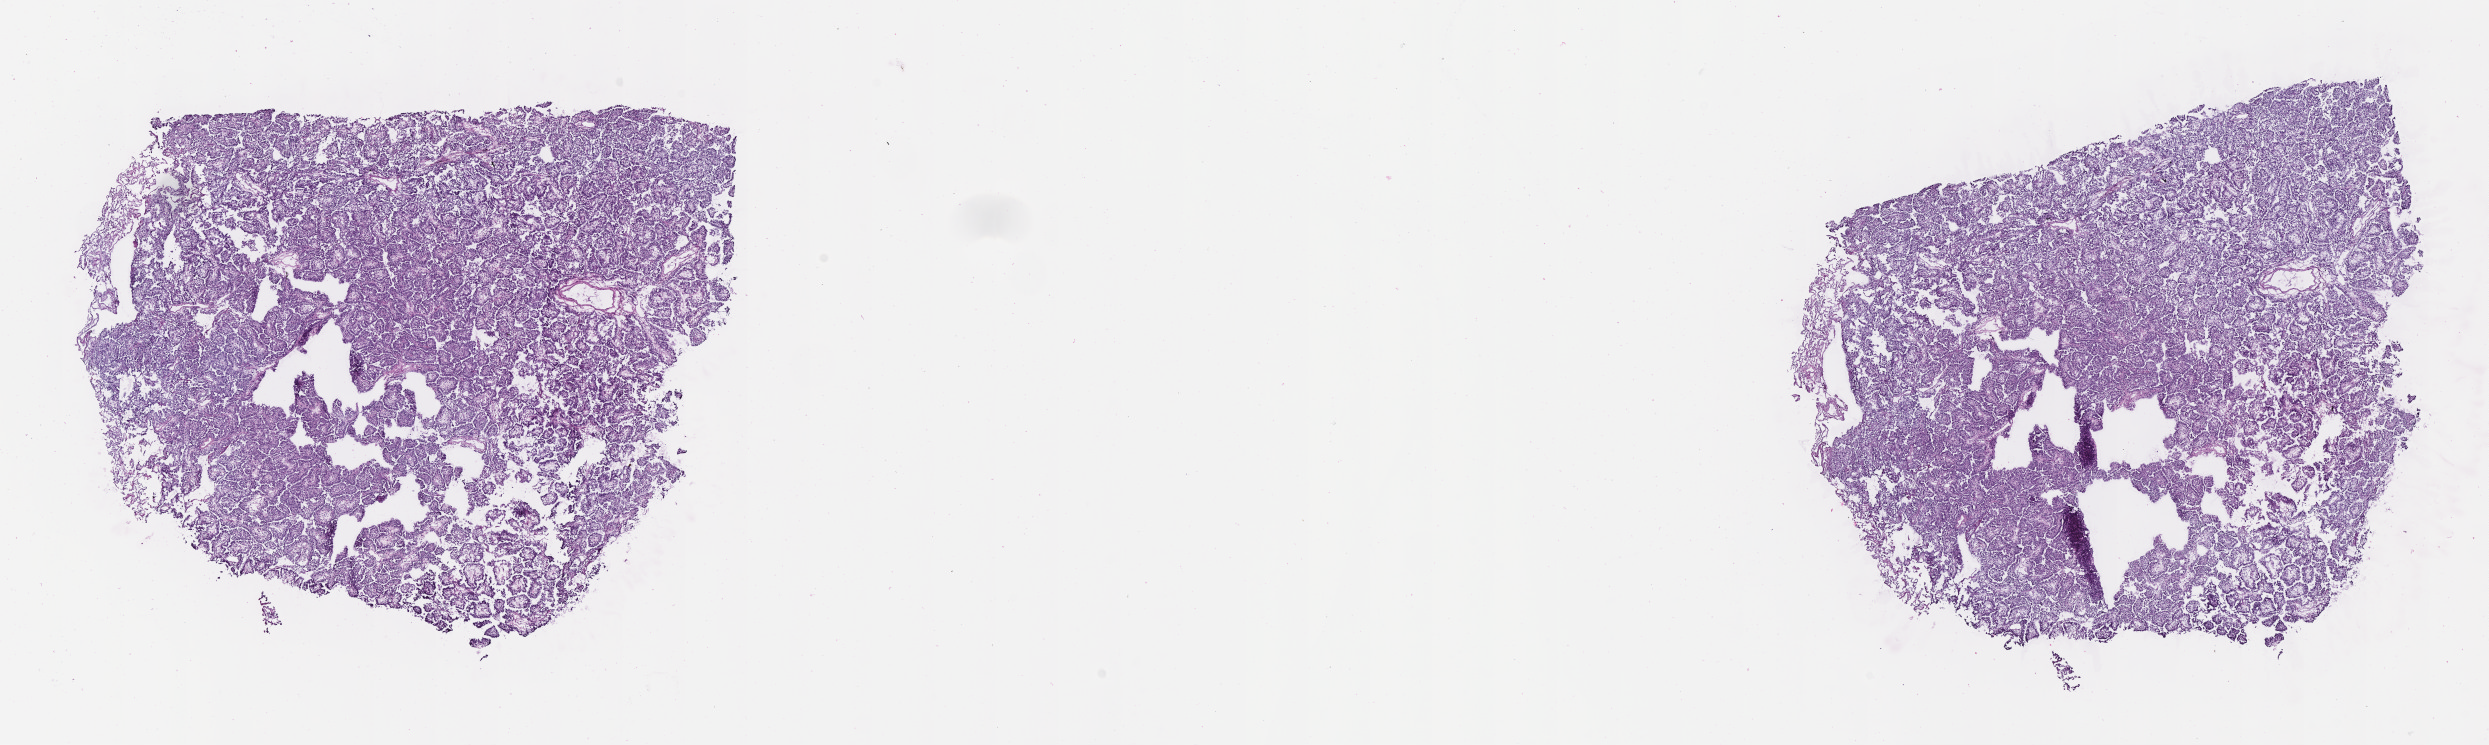
Digitized H&E-stained section — whole scanned area (about 20.1 x 6.0 mm) shown as a low-resolution overview. Frozen section (tissue freezing medium). Specimen: primary tumor. Site: upper lobe of right lung. Patient: male, age 68 years. Composition of this section per pathologist review: tumor cells 45%, tumor nuclei 85%, stromal cells 49%, necrosis 0%, normal cells 6%. Infiltration values recorded for this section: lymphocyte infiltration 4%, monocyte infiltration 4%, neutrophil infiltration 0%.
- diagnosis: Adenocarcinoma with mixed subtypes
- AJCC pathologic stage: Stage IB
- section: top of the tissue portion